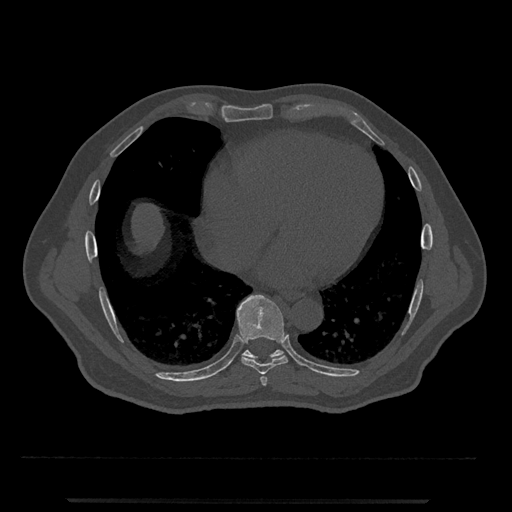
CT including the spine, one axial slice. Position 612 of 797 along the scan axis. 120 kVp. Bone window (W 1800 / L 400 HU). 512 × 512 image matrix, field of view 419 × 419 mm. Male patient, age 63 years. Case-level facts recorded for this patient, not image findings: primary cancer: prostate.
Structures marked on this image (semi-automatically segmented with operator editing):
- T7 vertebra: bounding box [x1, y1, x2, y2] px = [260, 376, 268, 386]
- T8 vertebra: [236, 295, 288, 375]
- T9 vertebra: [242, 350, 284, 361]